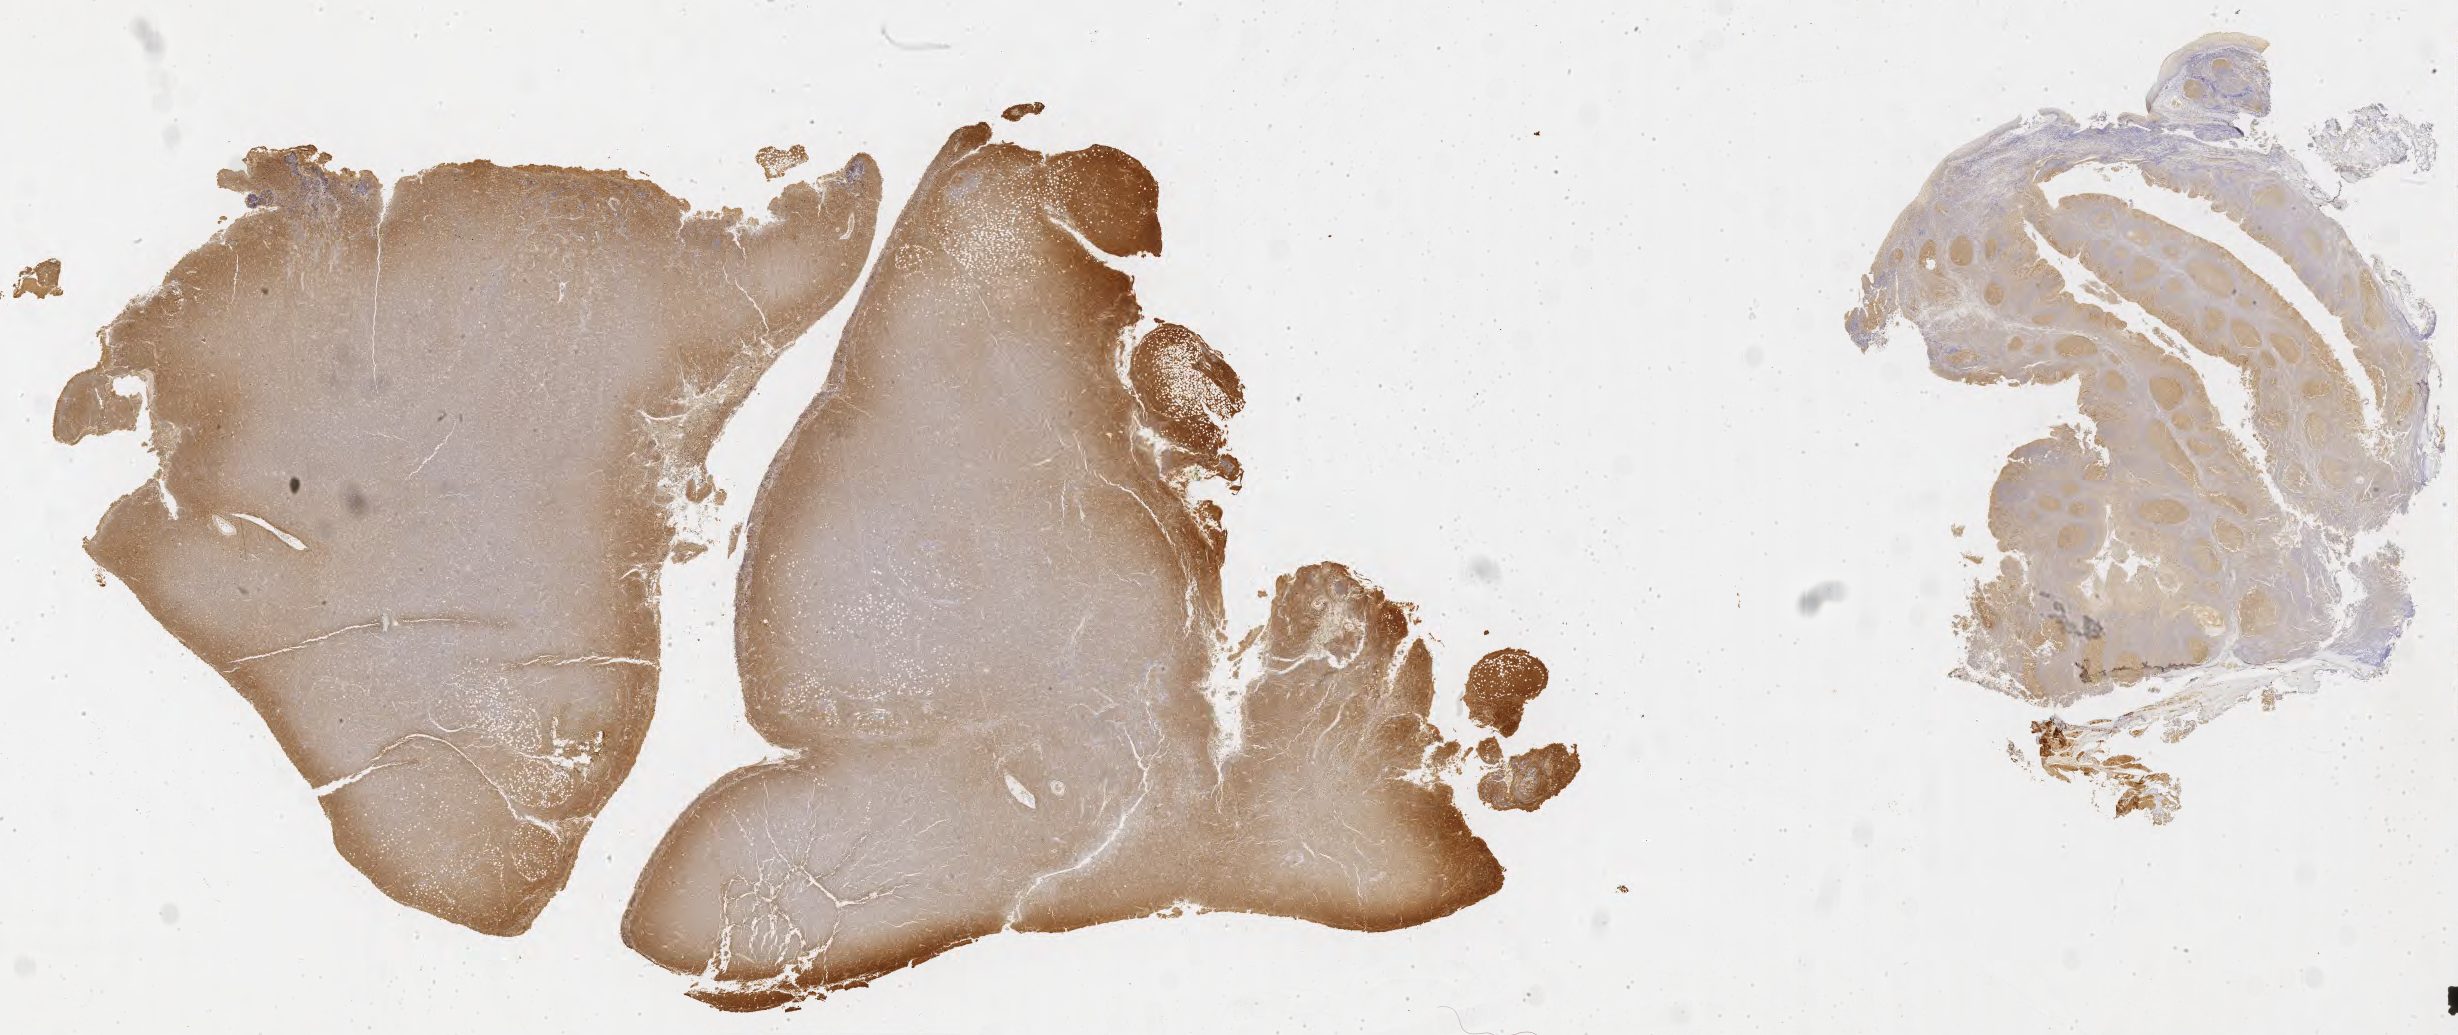
IHC for BCL6, whole-slide image, low-resolution overview of the scanned area, about 39.8 x 16.7 mm. Specimen: tumor tissue. Site: peritoneum. Male, age 9 years at initial diagnosis.
Diagnosis: Burkitt lymphoma, NOS.